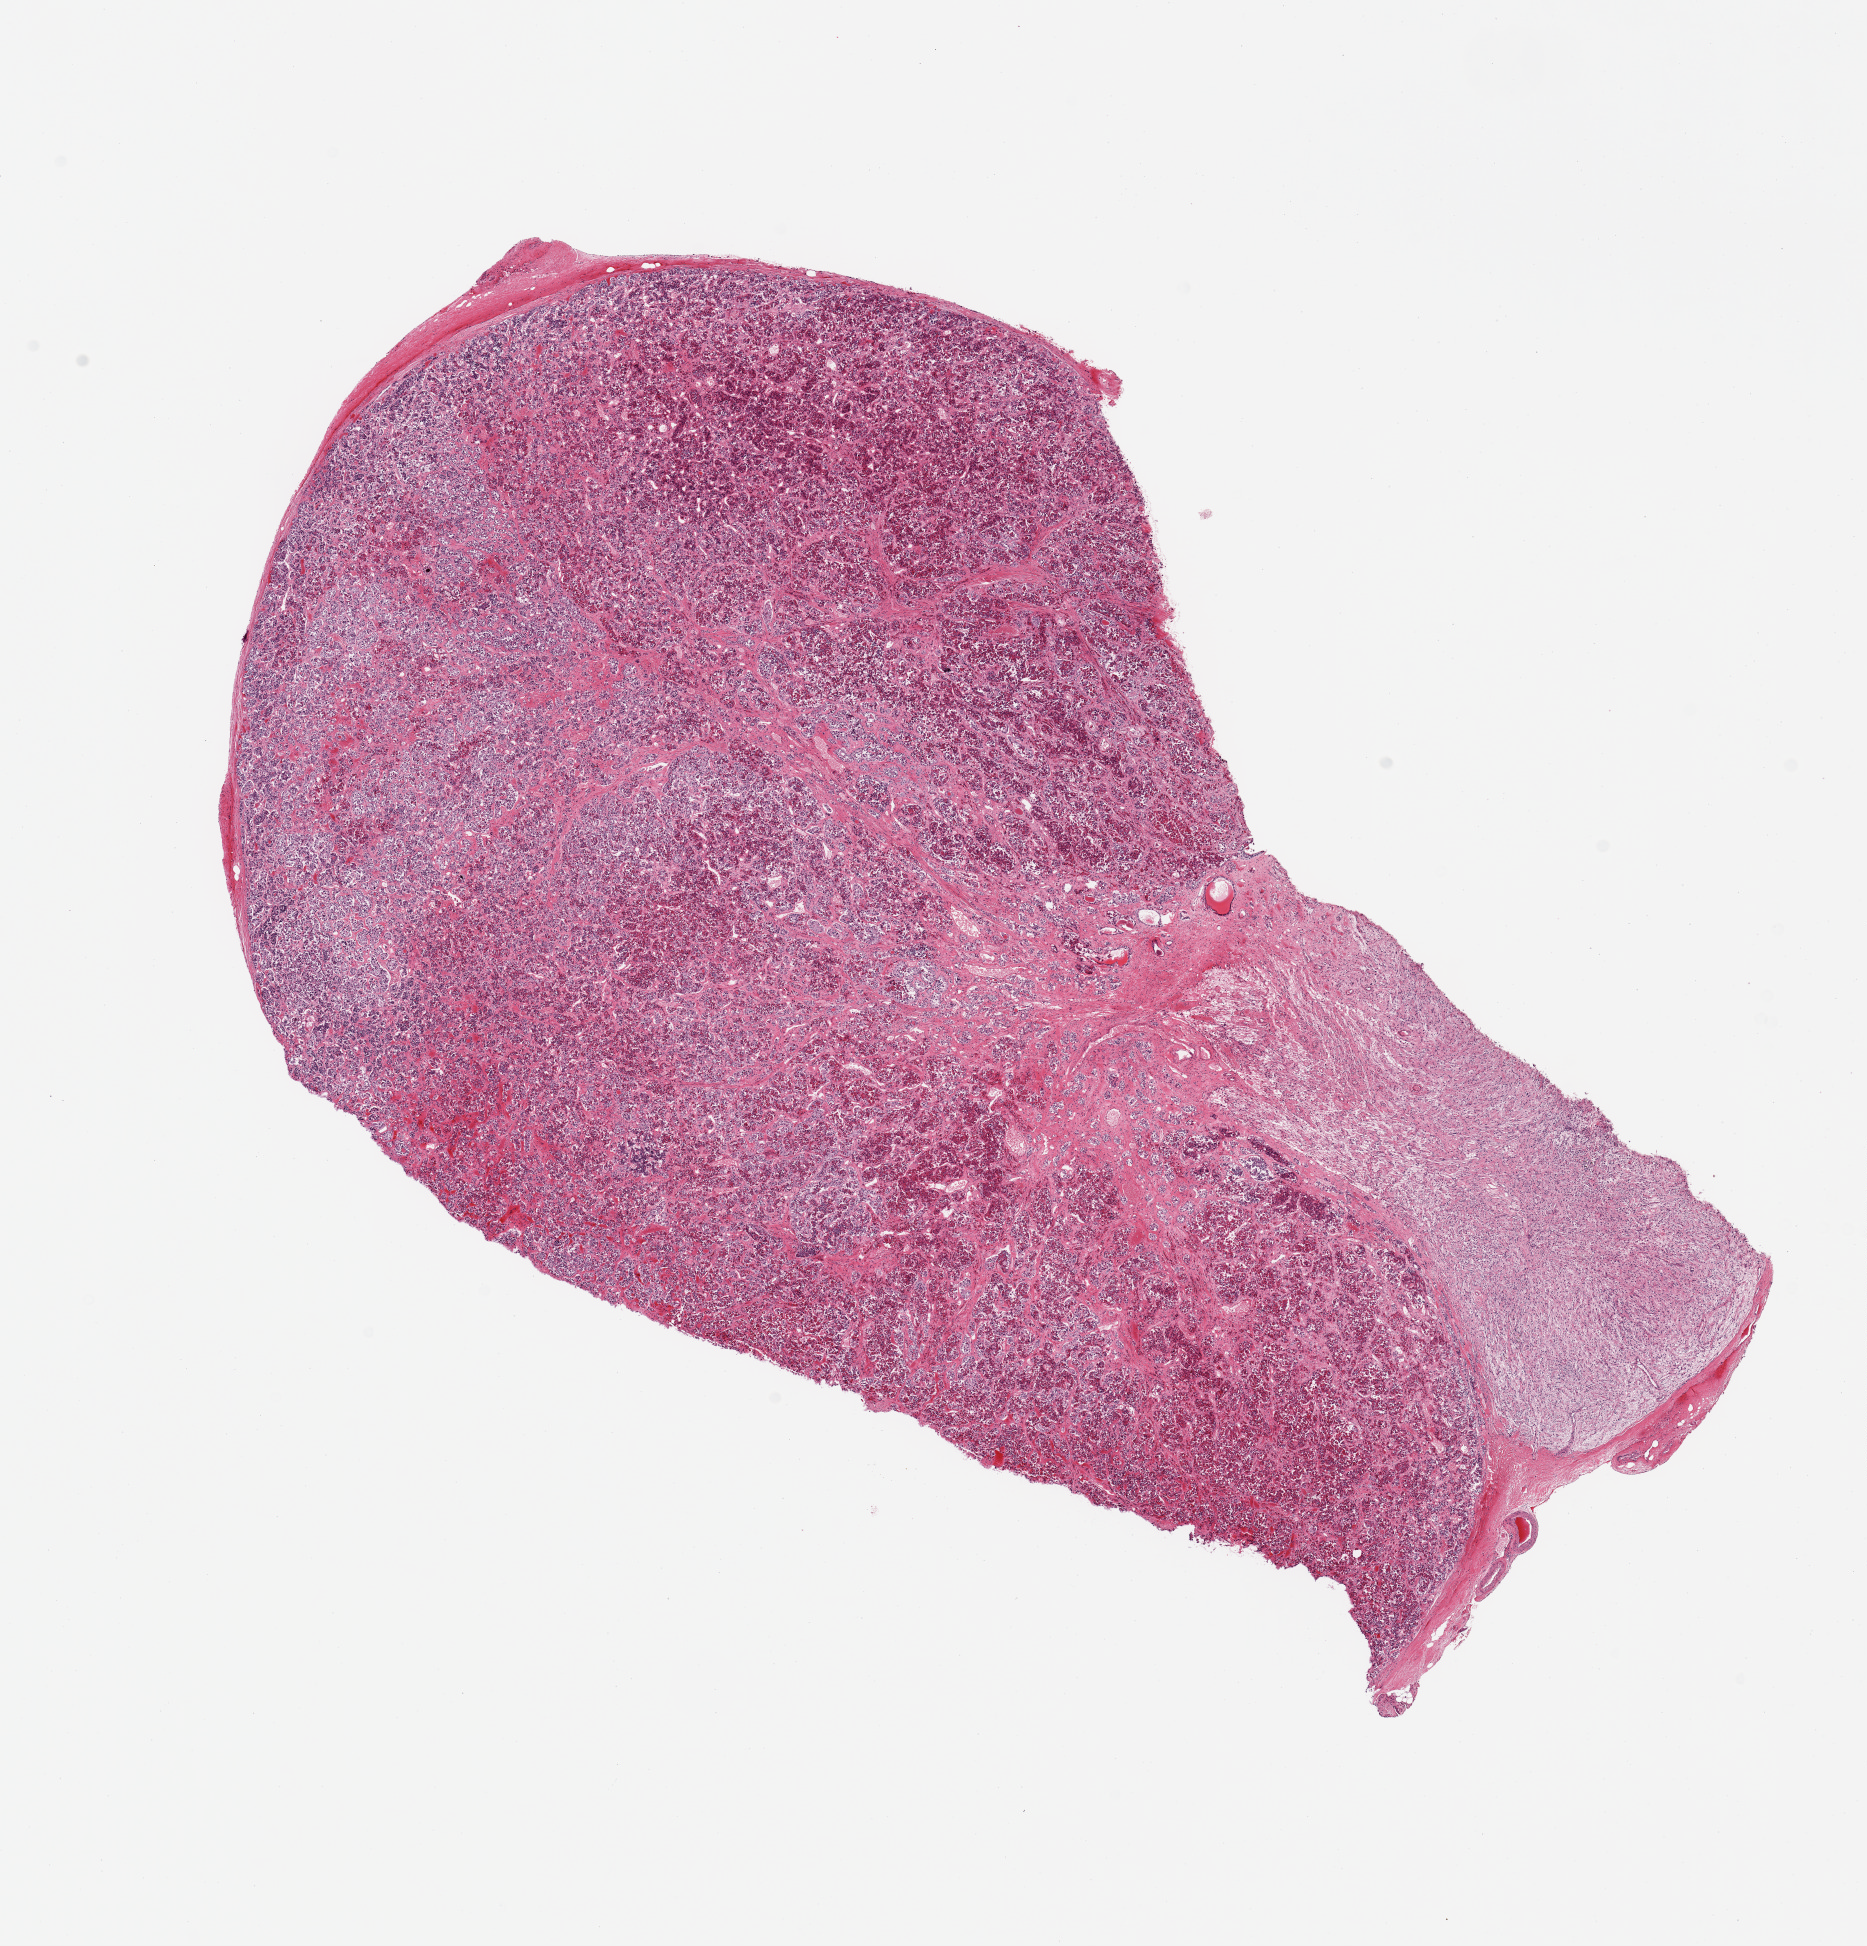
Whole-slide image, hematoxylin and eosin (H&E) stain — shown as a low-resolution overview of the whole scanned area (about 14.8 x 15.4 mm). PAXgene-fixed paraffin-embedded (PFPE) section. Section of pituitary (target tissue). Donor tissue sample. Male donor.
* pathologist's review note for this sample: 1 piece; 80% anterior; 20% posterior